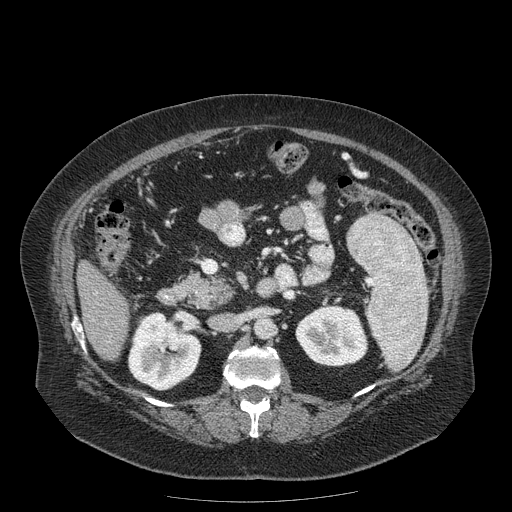
Contrast-enhanced abdominal CT (liver protocol), one axial slice. Slice 63 of 204 in the series (ordered by position). Reconstruction kernel STANDARD. Soft-tissue window (W 400 / L 40 HU). 2.5 mm slice thickness. 512 × 512 image matrix, field of view 440 × 440 mm. From the clinical record (not read from this slice): diagnosis: hepatocellular carcinoma (patient treated with transarterial chemoembolisation; whether this scan precedes or follows treatment is not stated here); TNM stage (as recorded): Stage-IIIB; Child-Pugh class: A; tumour differentiation: well differentiated; tumour nodularity: uninodular.
Outlined on this slice (semi-automatically segmented with operator editing):
- liver parenchyma outside the tumour (the mass and vessels are separate outlines, so this box may not span the whole liver): bounding box (x1, y1, x2, y2) in pixels: (76, 260, 128, 360)